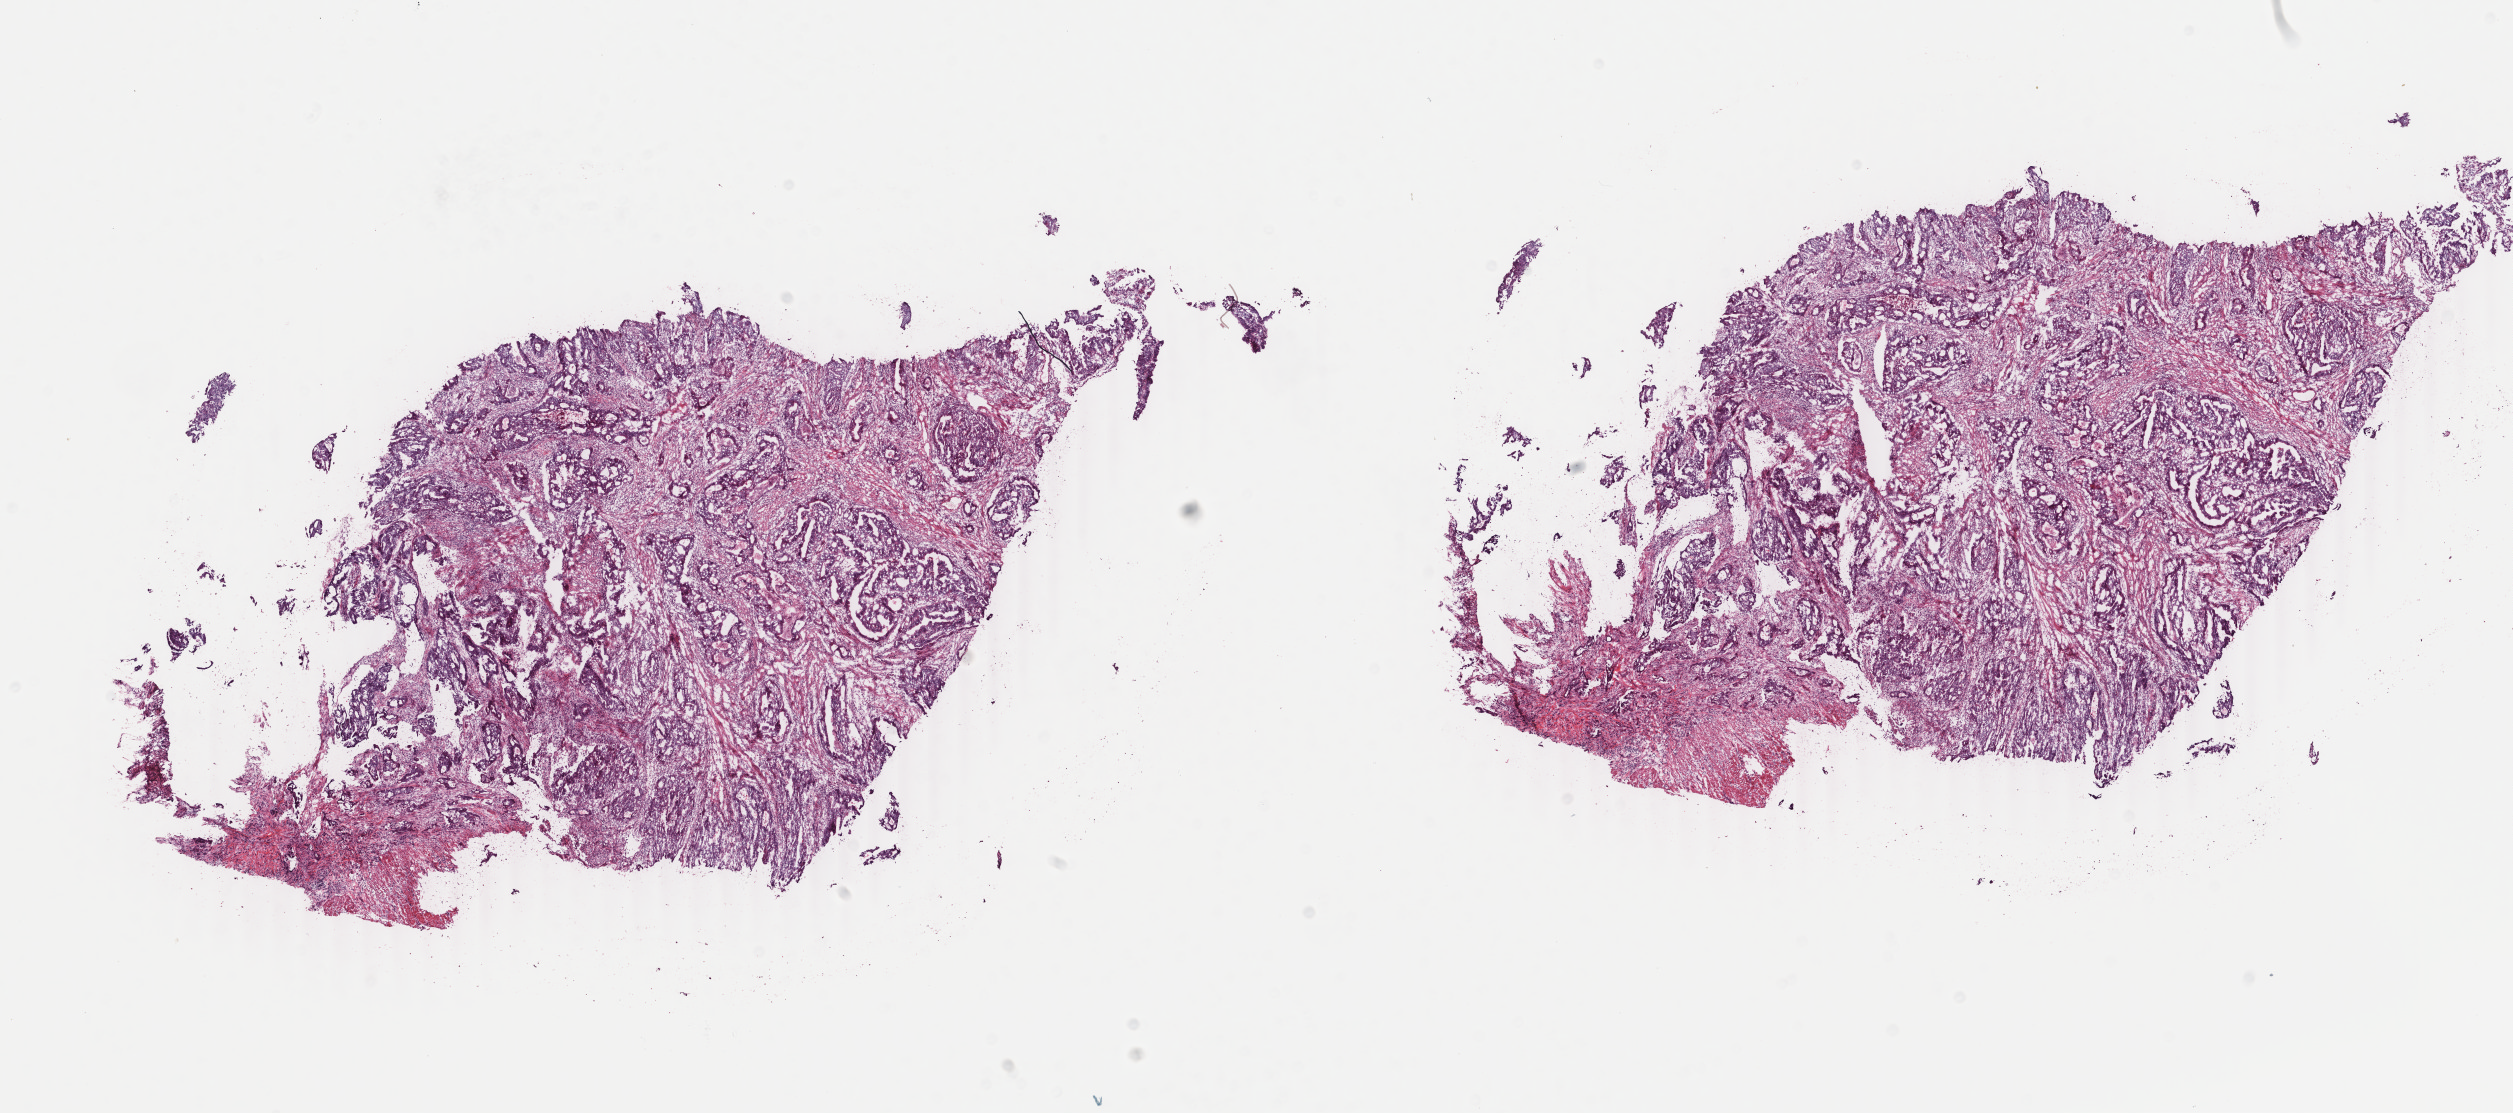
Whole-slide histology image, Hematoxylin and eosin (H&E) stained, whole scanned area (about 20.0 x 8.9 mm, slide scanned at 40x) shown as a low-resolution overview; frozen section from the top of the tissue portion; colon, primary tumour sample. Female, age 68 years at initial diagnosis. Slide review estimates, as recorded: tumour cells 76%, tumour nuclei 65%, normal cells 0%, stromal cells 20%, necrosis 4%. Inflammatory infiltration, as recorded: lymphocyte infiltration 6%, monocyte infiltration 1%, neutrophil infiltration 2%.
Pathologic diagnosis: Adenocarcinoma, NOS (sigmoid colon). AJCC pathologic stage: IIIC. Lymph nodes positive (case pathology): 4 of 22 examined.